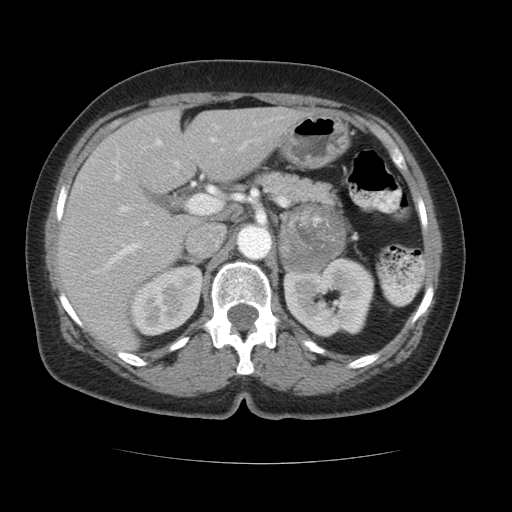
Contrast-enhanced abdominal CT, one axial slice; position 66 of 96 along the scan axis; 120 kVp; intravenous contrast given; soft-tissue window (W 400 / L 40 HU); 512 × 512 image matrix, field of view 348 × 348 mm. Female patient, age 66 years. Case-level facts recorded for this patient, not image findings: diagnosis: adrenocortical carcinoma; tumour side: left adrenal; tumour size at pathology: 5.5 cm; Ki-67 index: 15 %; stage (as recorded): 3.
Annotated regions visible in this slice (semi-automatically segmented with operator editing):
- mass: box from (x=279, y=204) to (x=342, y=271) px